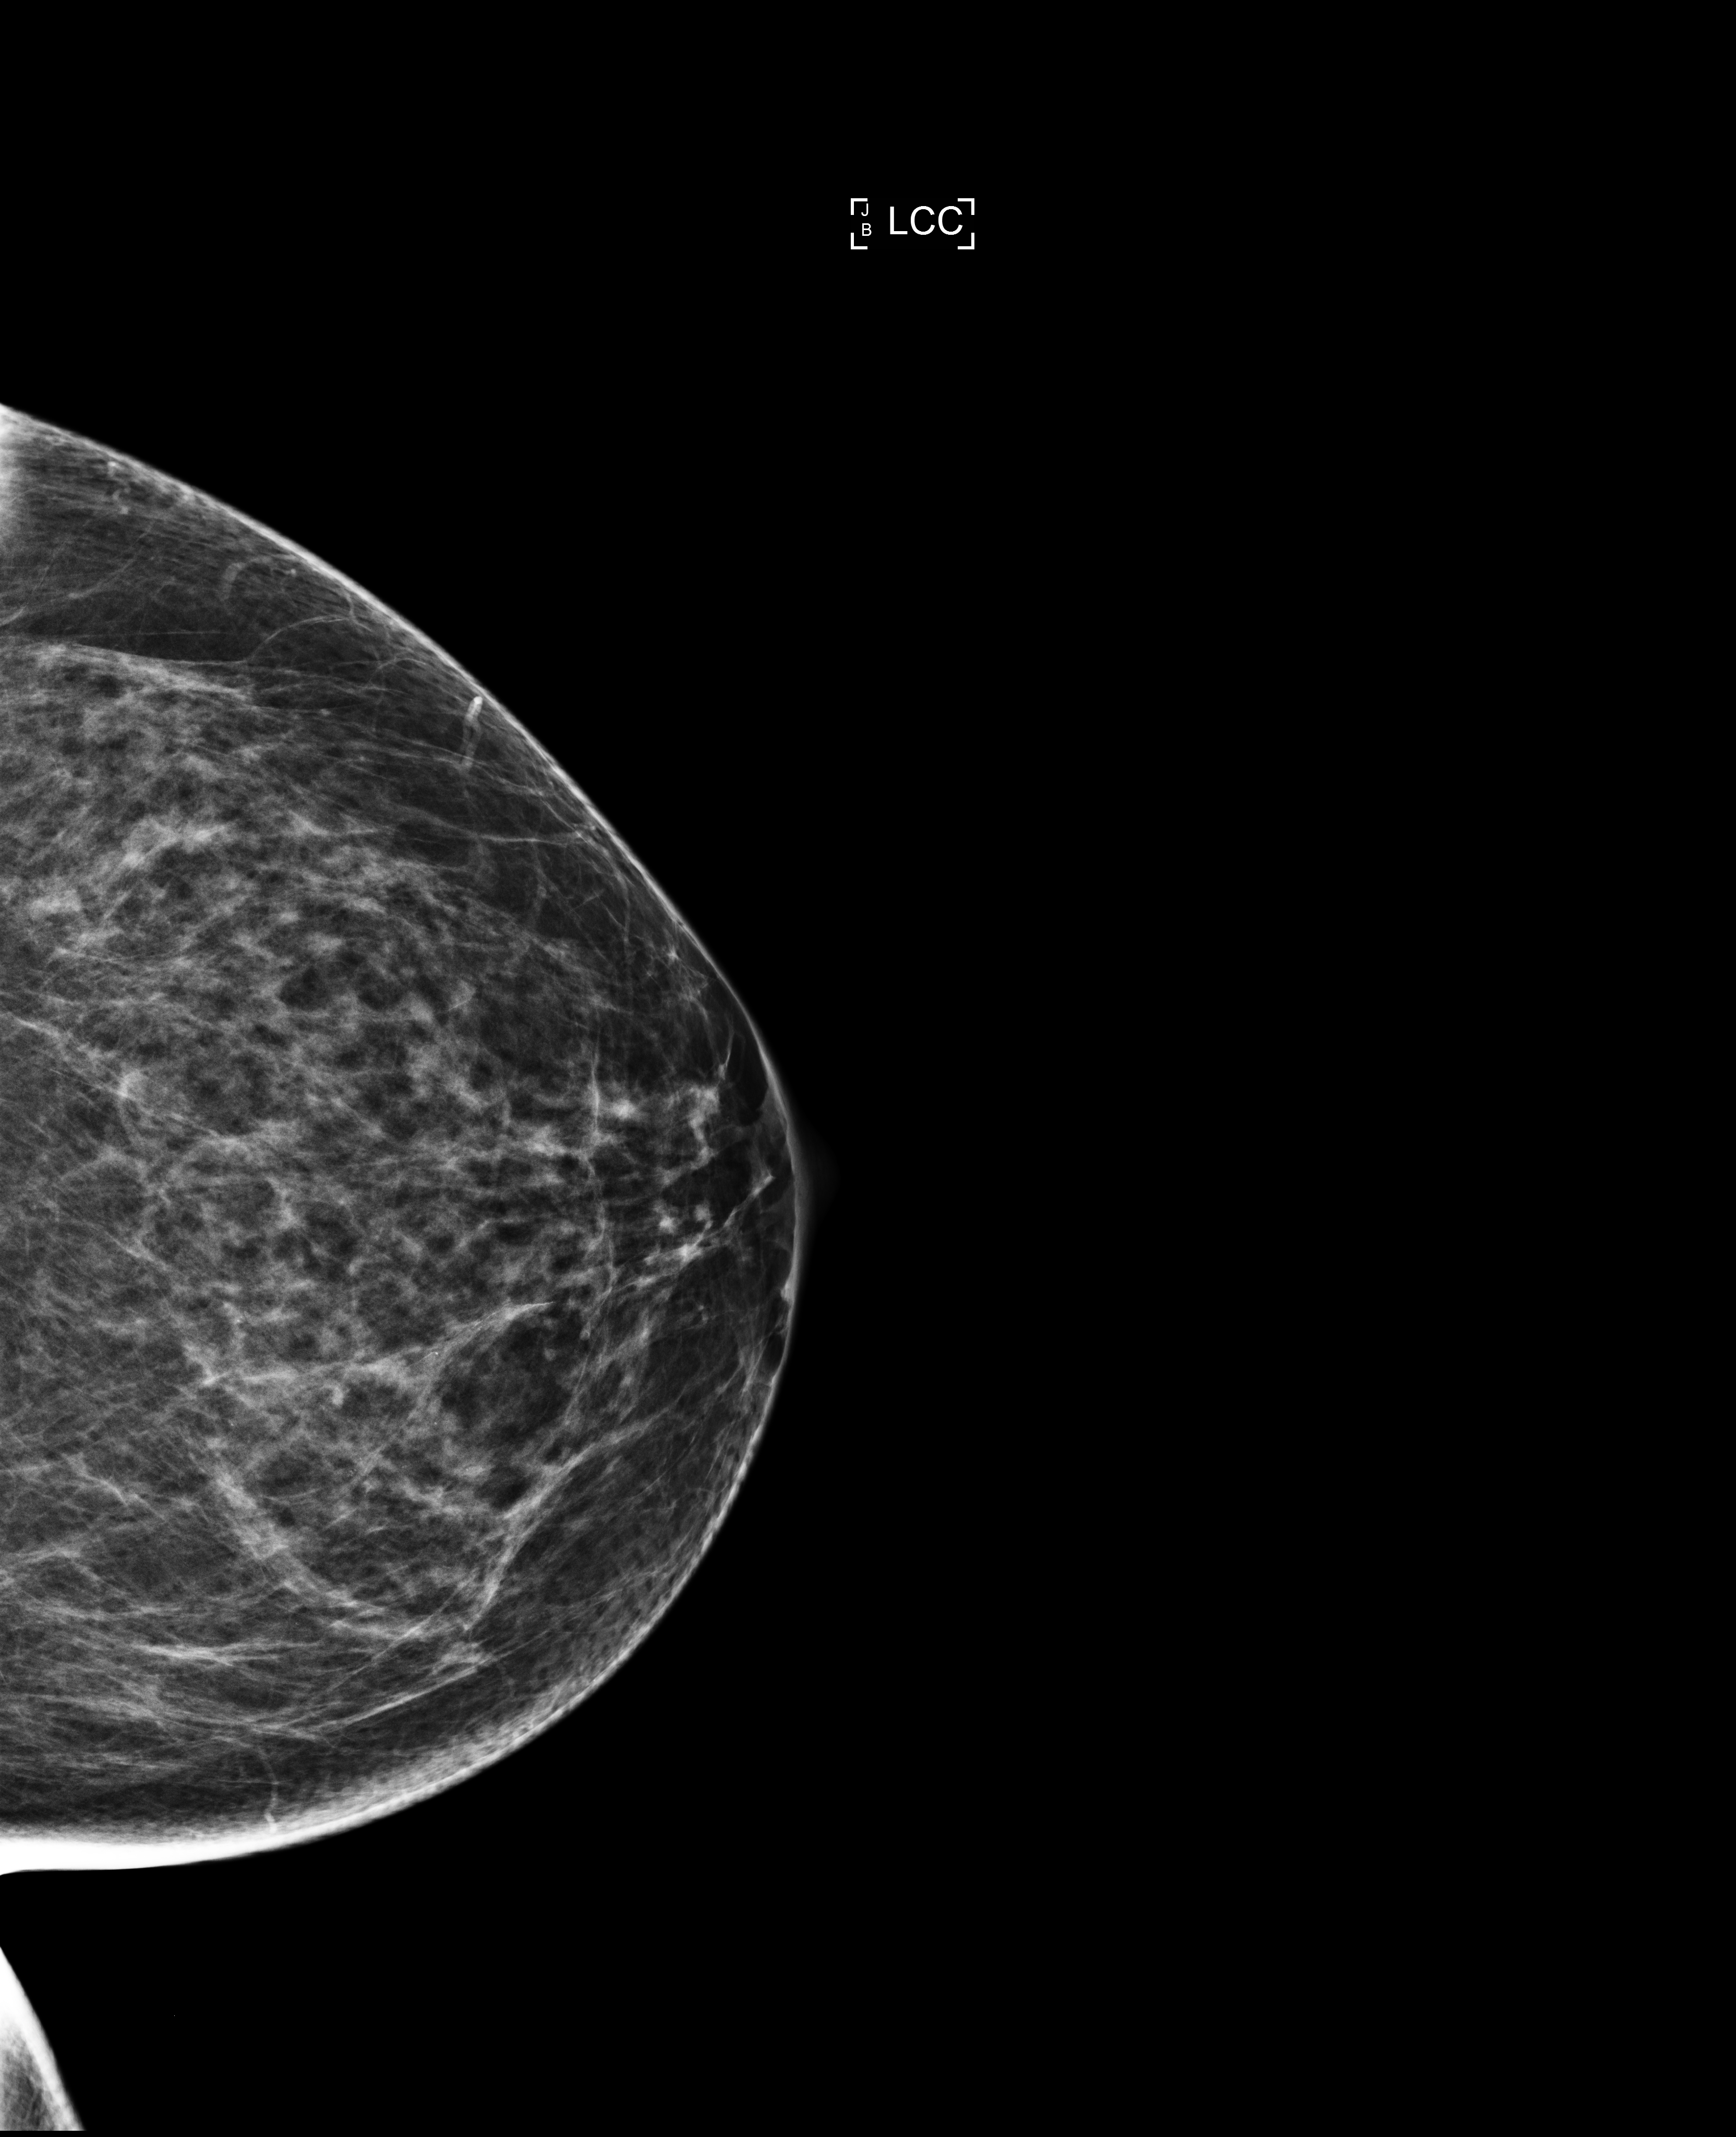
Digital mammogram (FFDM); left breast; craniocaudal (CC) view; screening examination. Patient aged 62 years (female).
- BI-RADS breast density category at the screening exam (both breasts, scale 1–4): 2
- final BI-RADS category for the screening round (tomosynthesis exam, both breasts): category 2
- recall: recalled for additional imaging after this screen